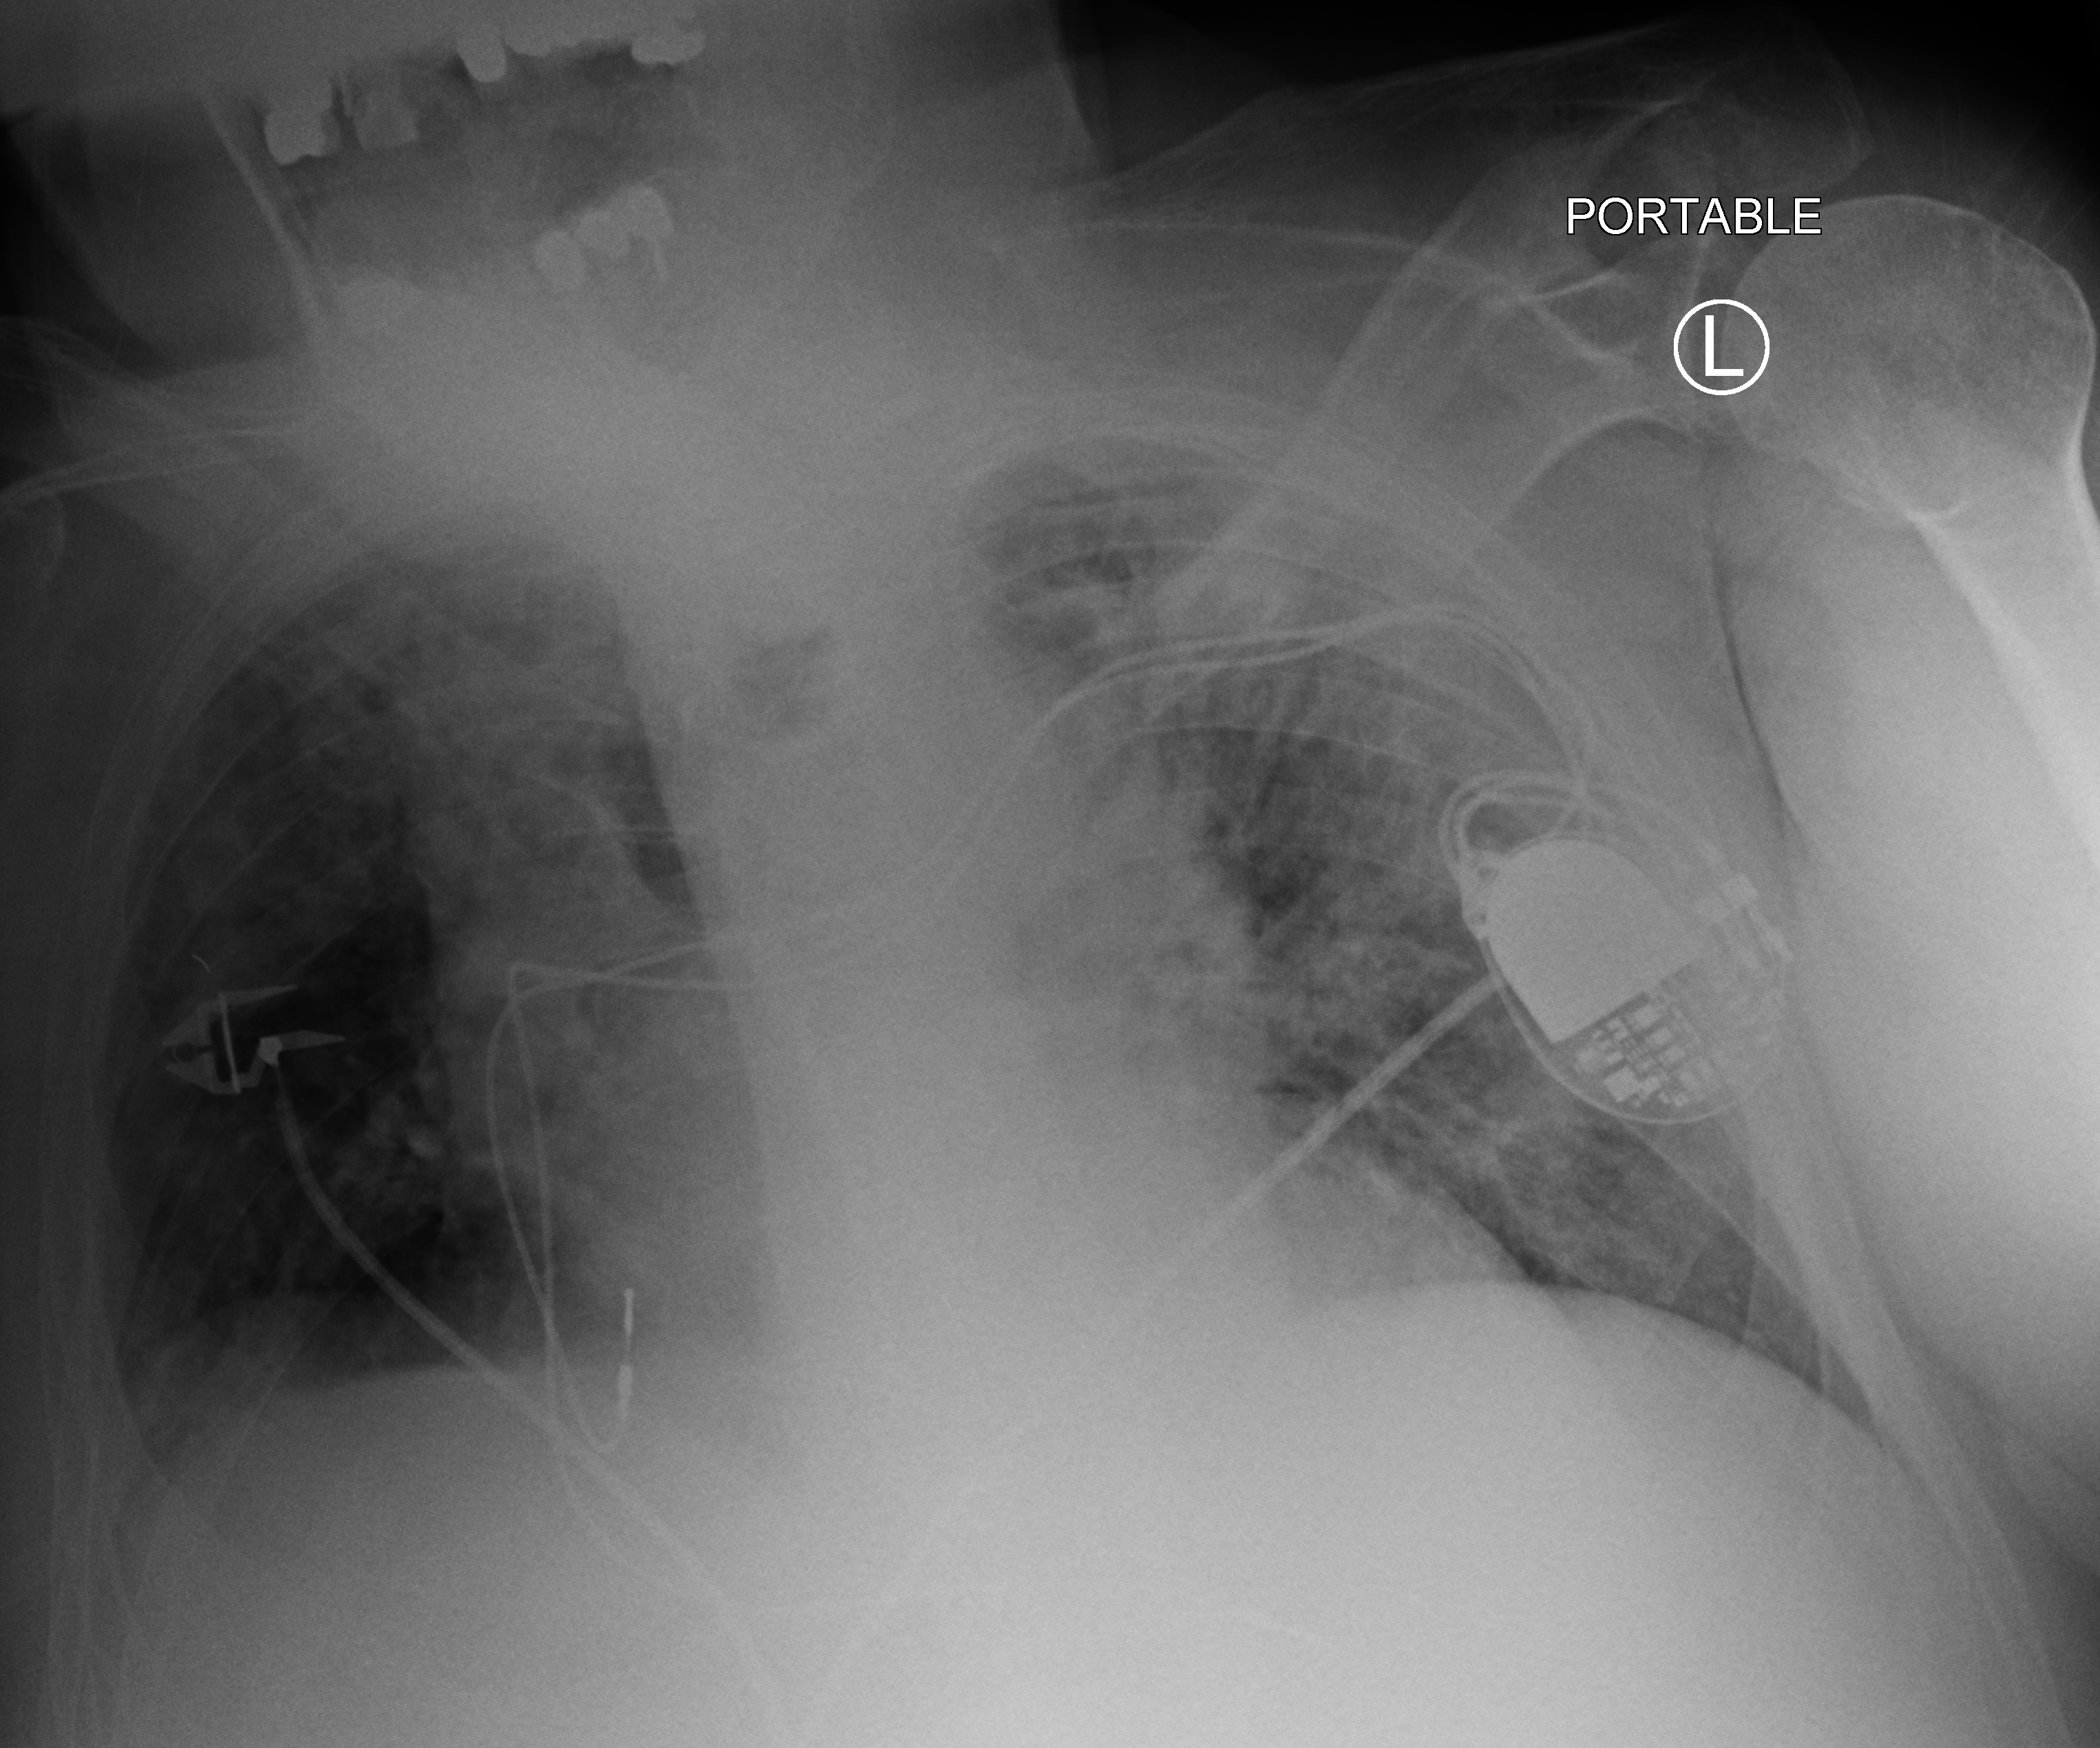
Chest X-ray (portable); anteroposterior (AP) projection. Male patient hospitalised with COVID-19, age 75–90 years.
Admission-level facts for this patient (not findings on this image; timing relative to this image not recorded): chronic kidney disease (admission record): no; mechanically ventilated during this hospital stay: no.